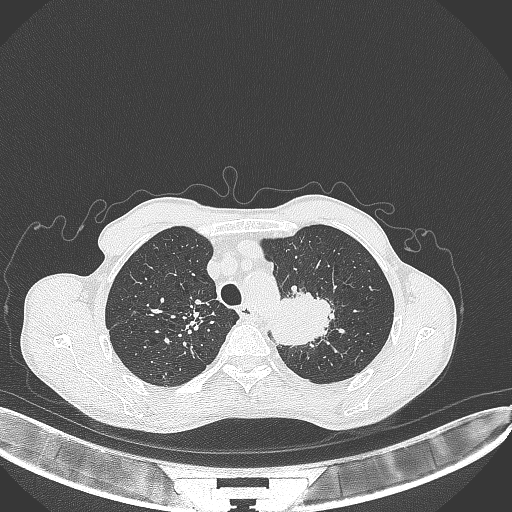
Chest CT, one axial slice. Slice 340 of 386 in the series (ordered by position). Lung window (W 1500 / L -600 HU). 1 mm slice thickness. 512 × 512 image matrix. Male patient, age 65 years. From the clinical record (not read from this slice): clinical TNM (as recorded): T2b N0 M0; histopathological grade: G2.
Annotated regions visible in this slice (bounding box drawn by a radiologist):
- lung tumour (recorded histology: adenocarcinoma): bounding box [x1, y1, x2, y2] px = [265, 289, 334, 344]